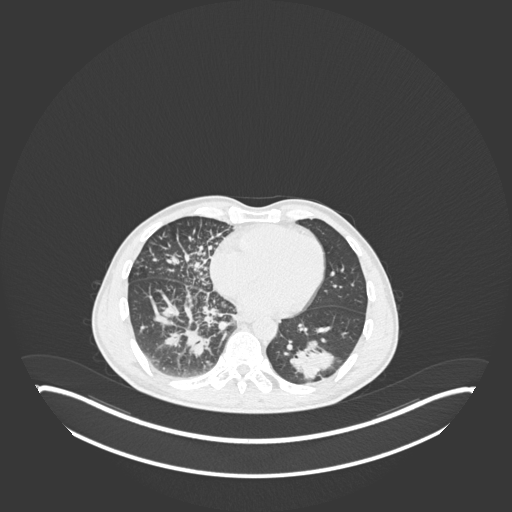
Chest CT, one axial slice; position 83 of 237 along the scan axis; reconstruction kernel B30f; 120 kVp; lung window (W 1500 / L -600 HU); 1 mm slice thickness; 512 × 512 image matrix. Patient: male, 49 years. Case-level facts recorded for this patient, not image findings: clinical TNM (as recorded): T2b N1 M0.
Structures marked on this image (bounding box drawn by a radiologist):
- lung tumour (recorded histology: adenocarcinoma): bounding box <287,337,341,382> (left, top, right, bottom; pixels)